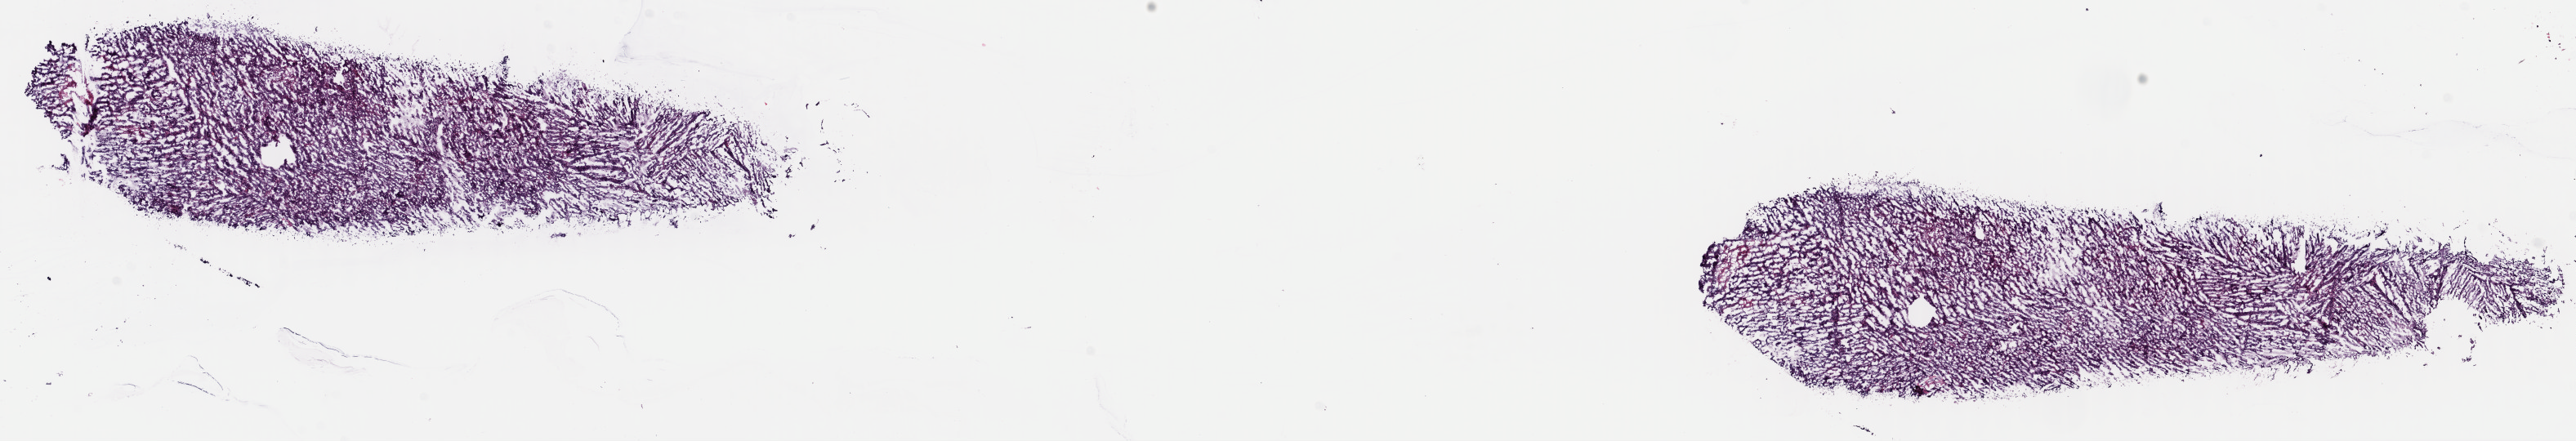
Digitized H&E tissue section (whole slide), shown as a low-resolution overview of the whole scanned area (about 24.8 x 4.2 mm); frozen section from the top of the tissue portion; primary tumour sample from the uterus. Female patient; age at initial diagnosis 63 years. Histologic grade: G3 (poorly differentiated). Composition of this section per pathologist review: tumour cells 80%, tumour nuclei 80%, normal cells 0%, stromal cells 10%, necrosis 10%. Infiltration values recorded for this section: lymphocyte infiltration 40%, monocyte infiltration 10%, neutrophil infiltration 30%.
FIGO stage: IIIC. Lymph nodes positive (case pathology): 2 of 9 examined. Histologic diagnosis: Serous cystadenocarcinoma, NOS.